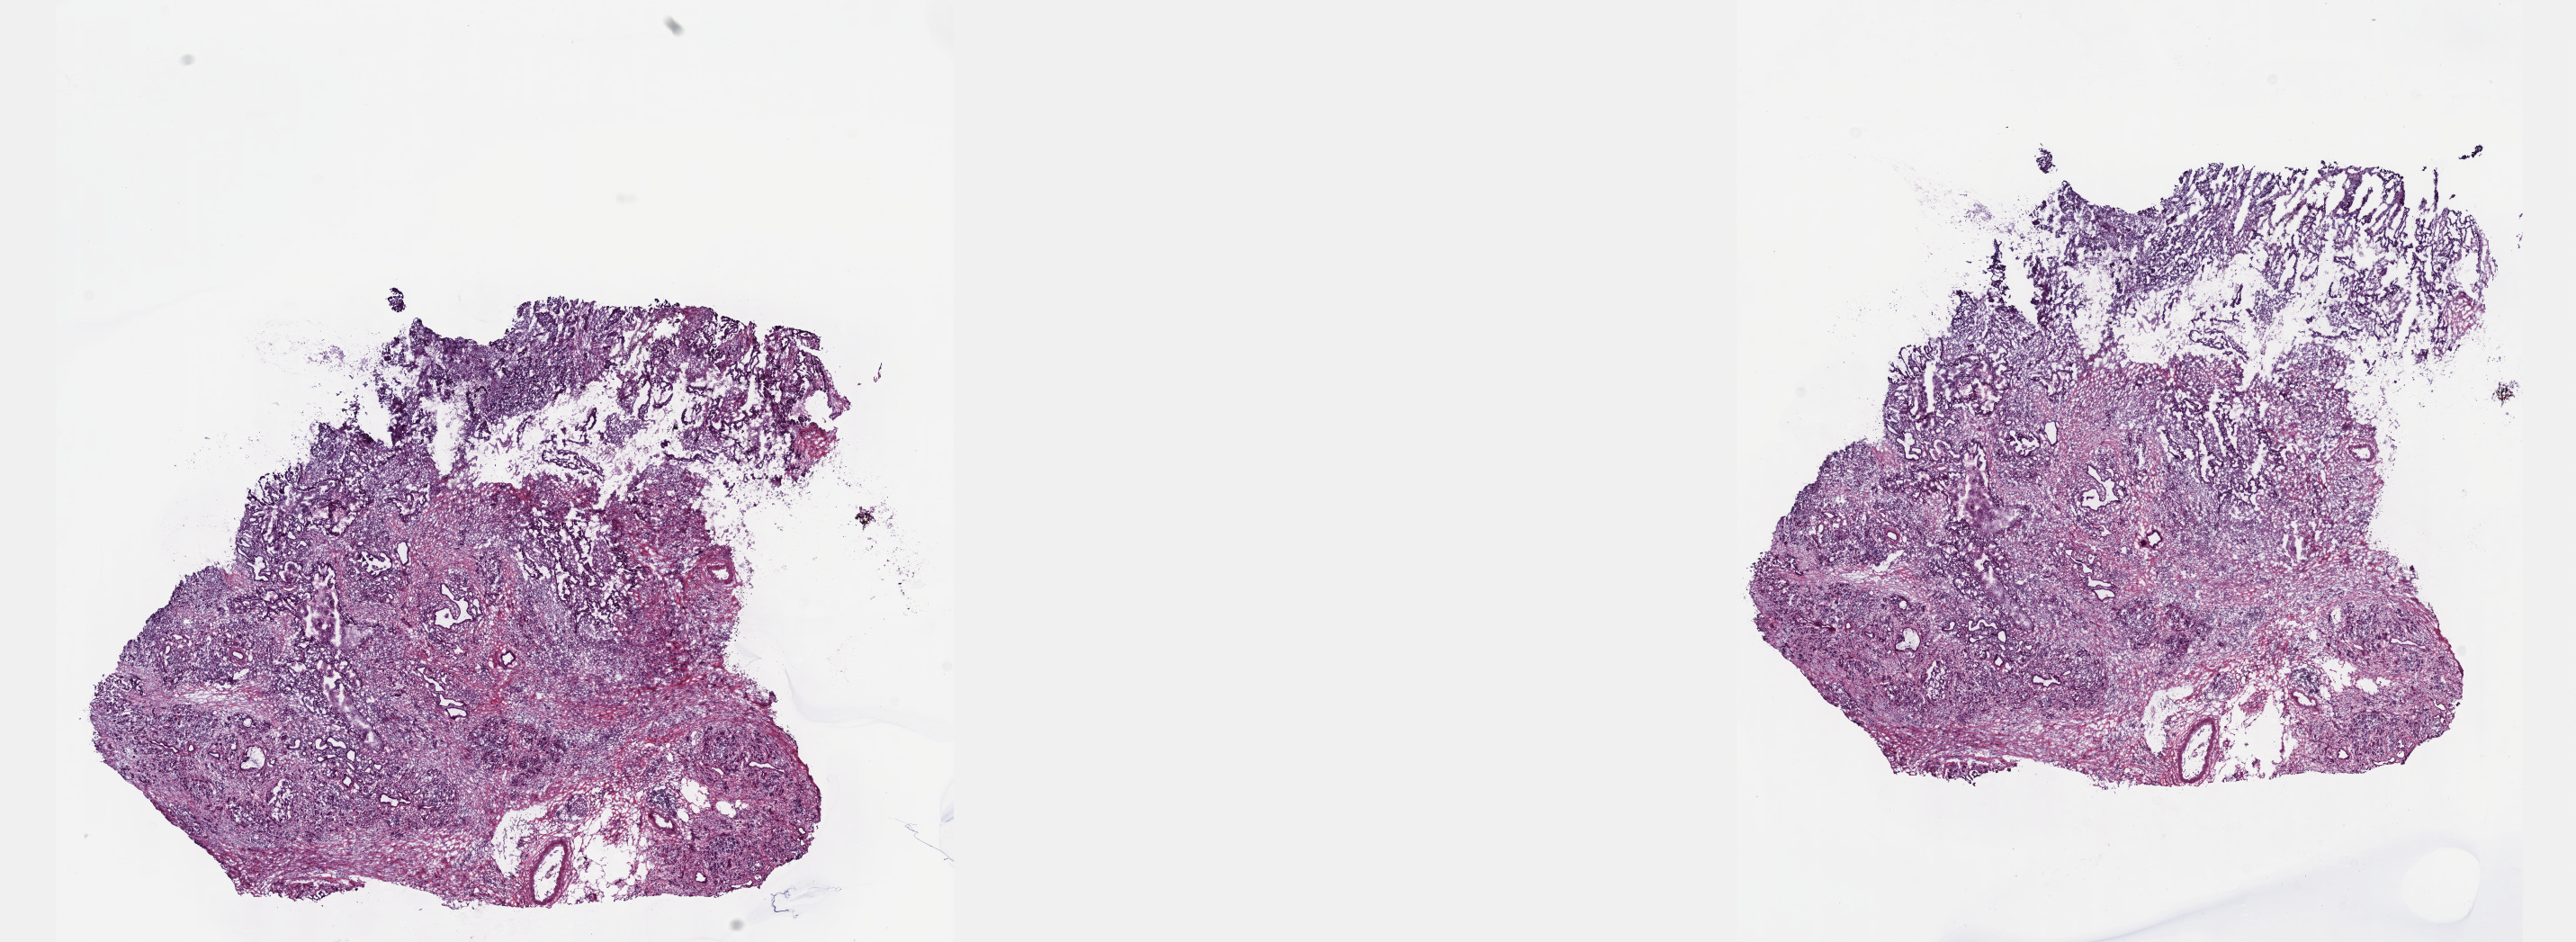
Digitized Hematoxylin and eosin (H&E) stained tissue section (whole slide), shown as a low-resolution overview of the whole scanned area (about 23.1 x 8.5 mm). Frozen section from the top of the tissue portion. Sample: primary tumour, pancreas. Patient: female, age at initial diagnosis 64 years. Histologic grade: G3 (poorly differentiated). Pathologist review of this section (percent, as recorded): tumour cells 20%, tumour nuclei 20%, normal cells 35%, stromal cells 45%, necrosis 0%. Inflammatory infiltration, as recorded: lymphocyte infiltration 3%, monocyte infiltration 1%, neutrophil infiltration 5%.
AJCC pathologic stage: IIB (7th edition). Histologic diagnosis: Infiltrating duct carcinoma, NOS. Lymph nodes positive (case pathology): 5 of 5 examined.